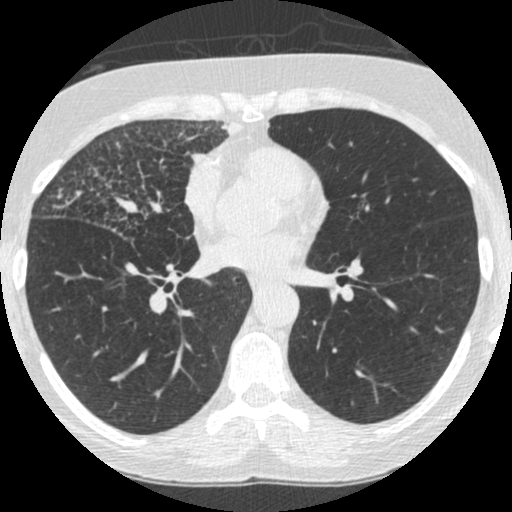
Low-dose screening chest CT, one axial slice. Reconstruction kernel STANDARD. 120 kVp. Lung window (W 1500 / L -600 HU). 1.25 mm slice thickness. 512 × 512 image matrix.
Structures marked on this image (manually delineated by an expert):
- lesion 4 (tumor, upper lobe of right lung): bounding box (x1, y1, x2, y2) in pixels: (197, 117, 242, 155)